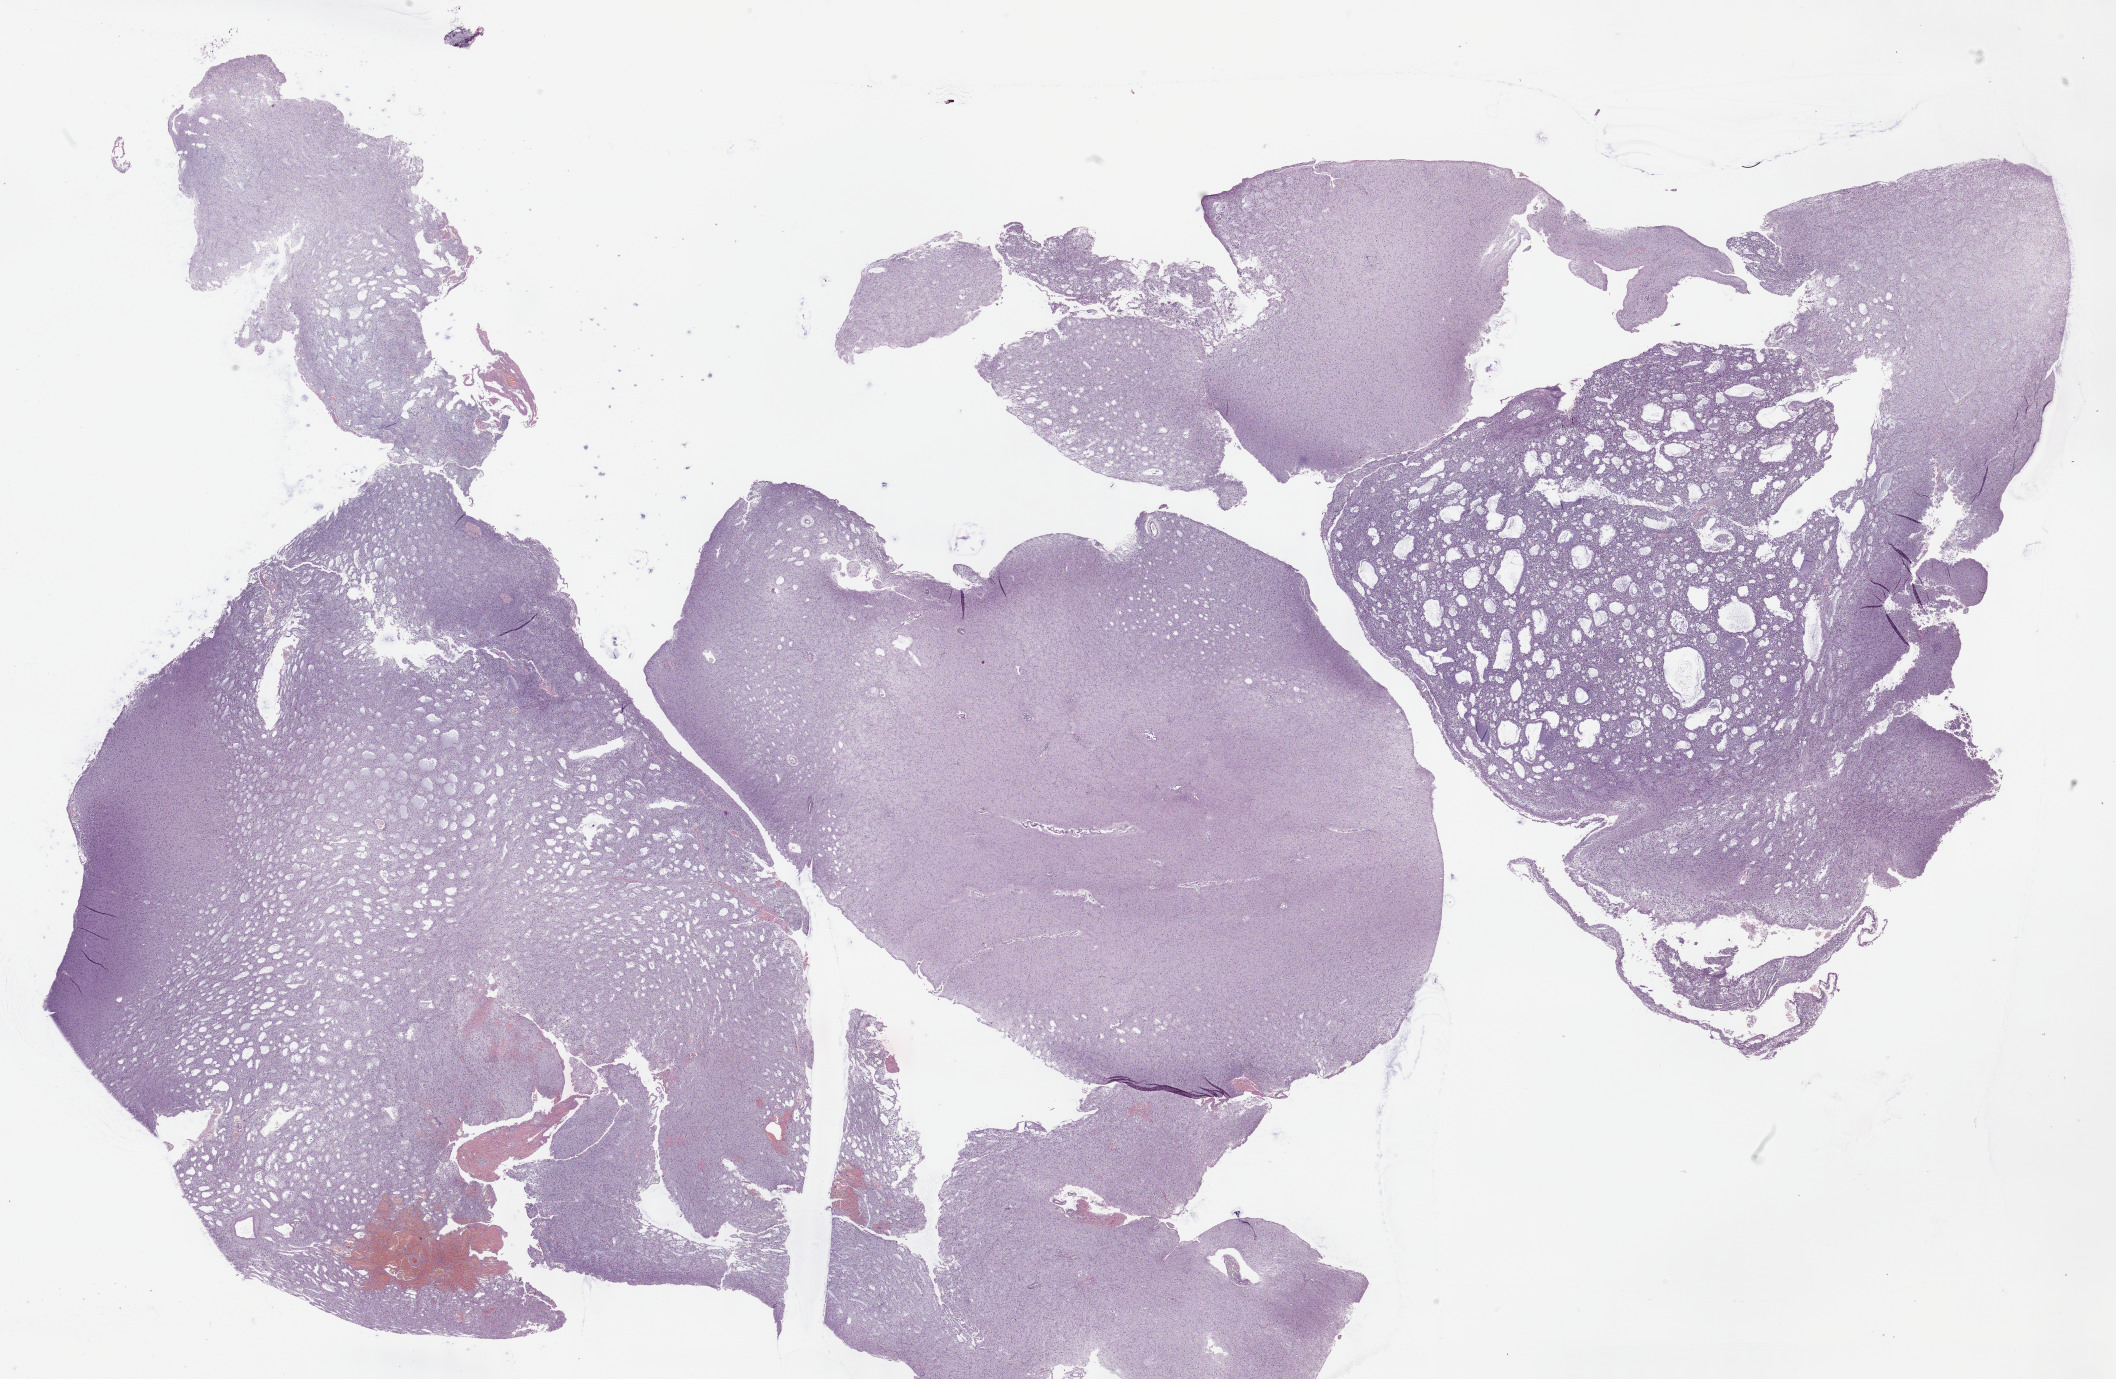
Hematoxylin and eosin (H&E) stained whole-slide image, a low-resolution overview of the entire scanned area, about 34.2 x 22.3 mm (acquisition: 40x scan). FFPE section. Sample: primary tumour, brain. Female patient; age at initial diagnosis 44 years. Histologic grade: G3 (poorly differentiated).
Histologic diagnosis: Astrocytoma, anaplastic.